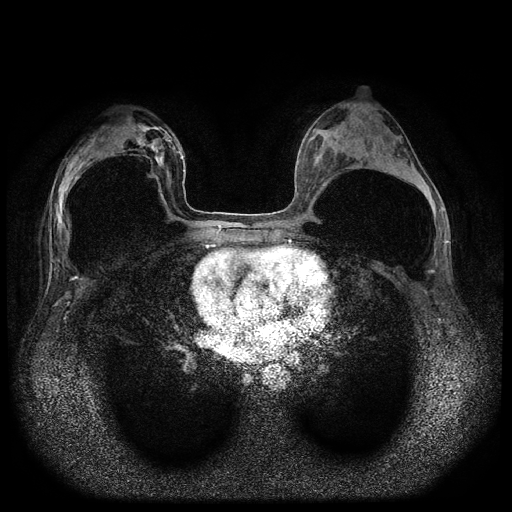
Breast MRI (dynamic contrast-enhanced, multi-phase), one axial slice. Slice 44 of 116 in the series (ordered by position). Dynamic contrast-enhanced series, time point 2 of 5 at this slice position (early post-contrast). 1.5 T. TE 2.6 ms, TR 5.4 ms. 2 mm slice thickness. 512 × 512 image matrix, field of view 340 × 340 mm. Female patient, age 42 years.
Outlined on this slice (semi-automatically segmented with operator editing):
- breast lesion (labelled 'tumour' in the annotation; benign lesions carry a separate 'benign' label): bounding box <136,126,167,167> (left, top, right, bottom; pixels)